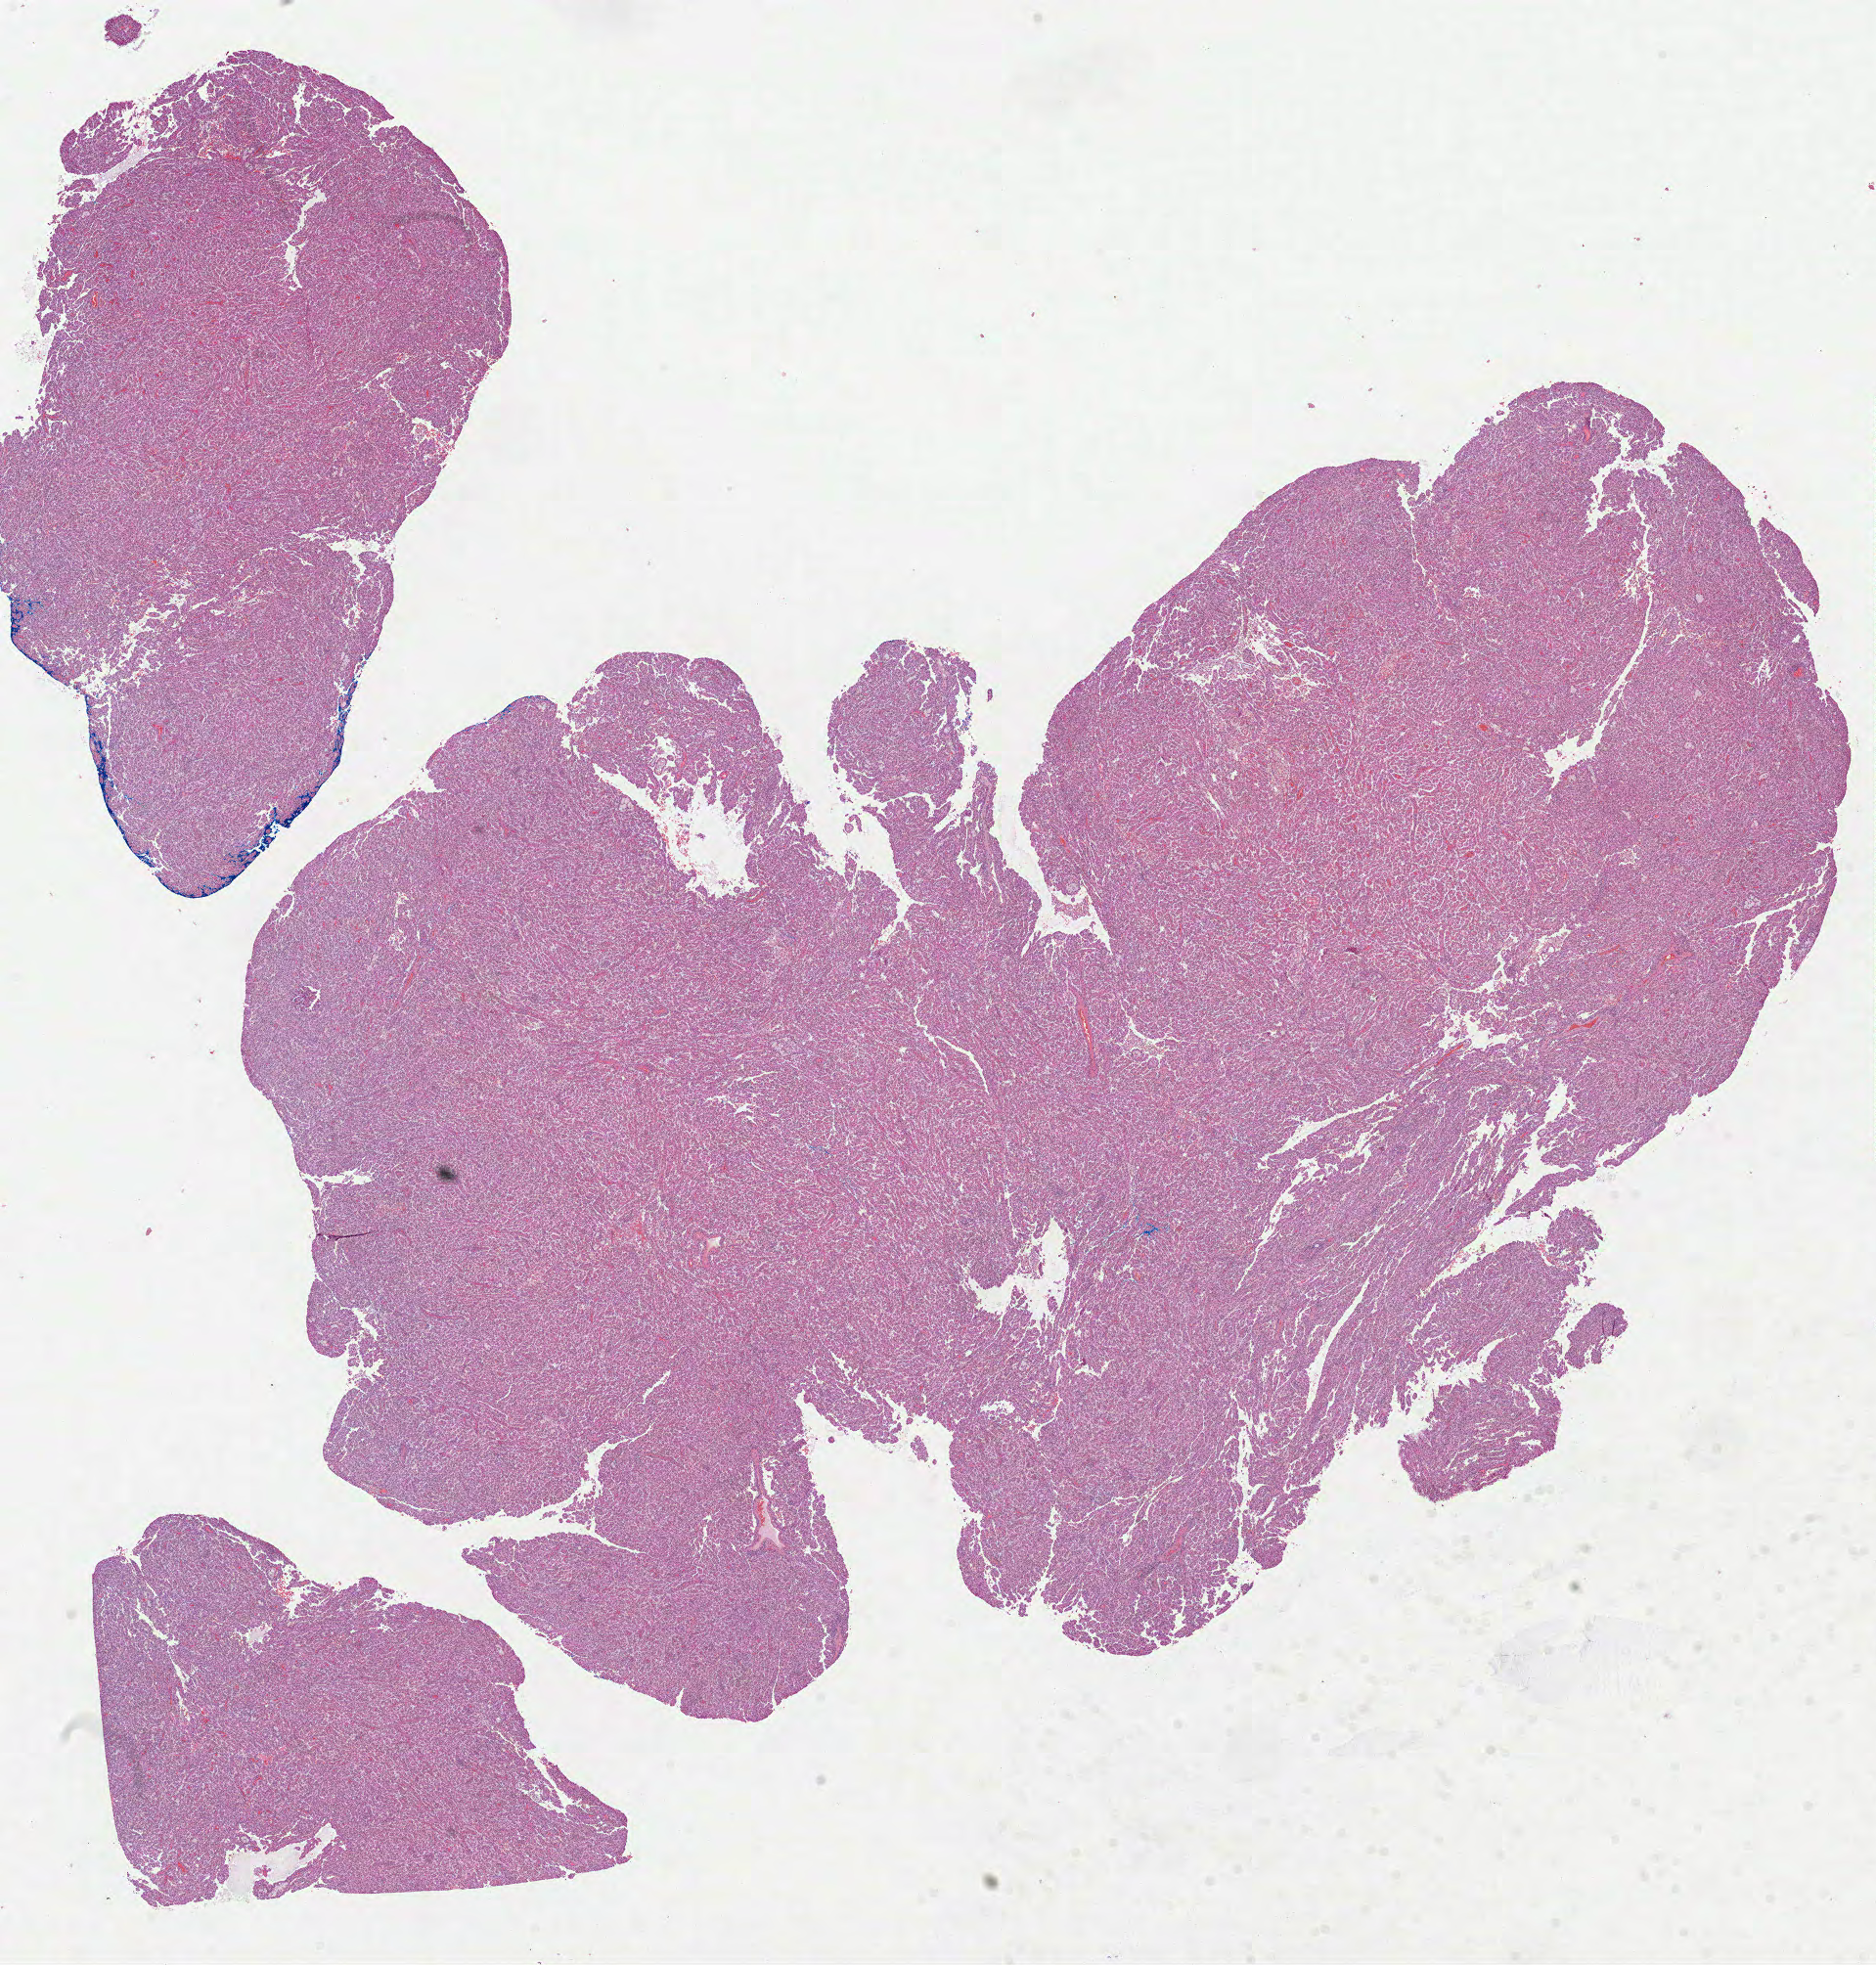
Whole-slide histology image, H&E — whole scanned area (about 15.5 x 16.2 mm, from a 40x scan) shown as a low-resolution overview, formalin-fixed paraffin-embedded (FFPE) diagnostic section, primary tumour sample from the kidney. Male, age 60 years at initial diagnosis.
Pathologic diagnosis: Papillary adenocarcinoma, NOS.